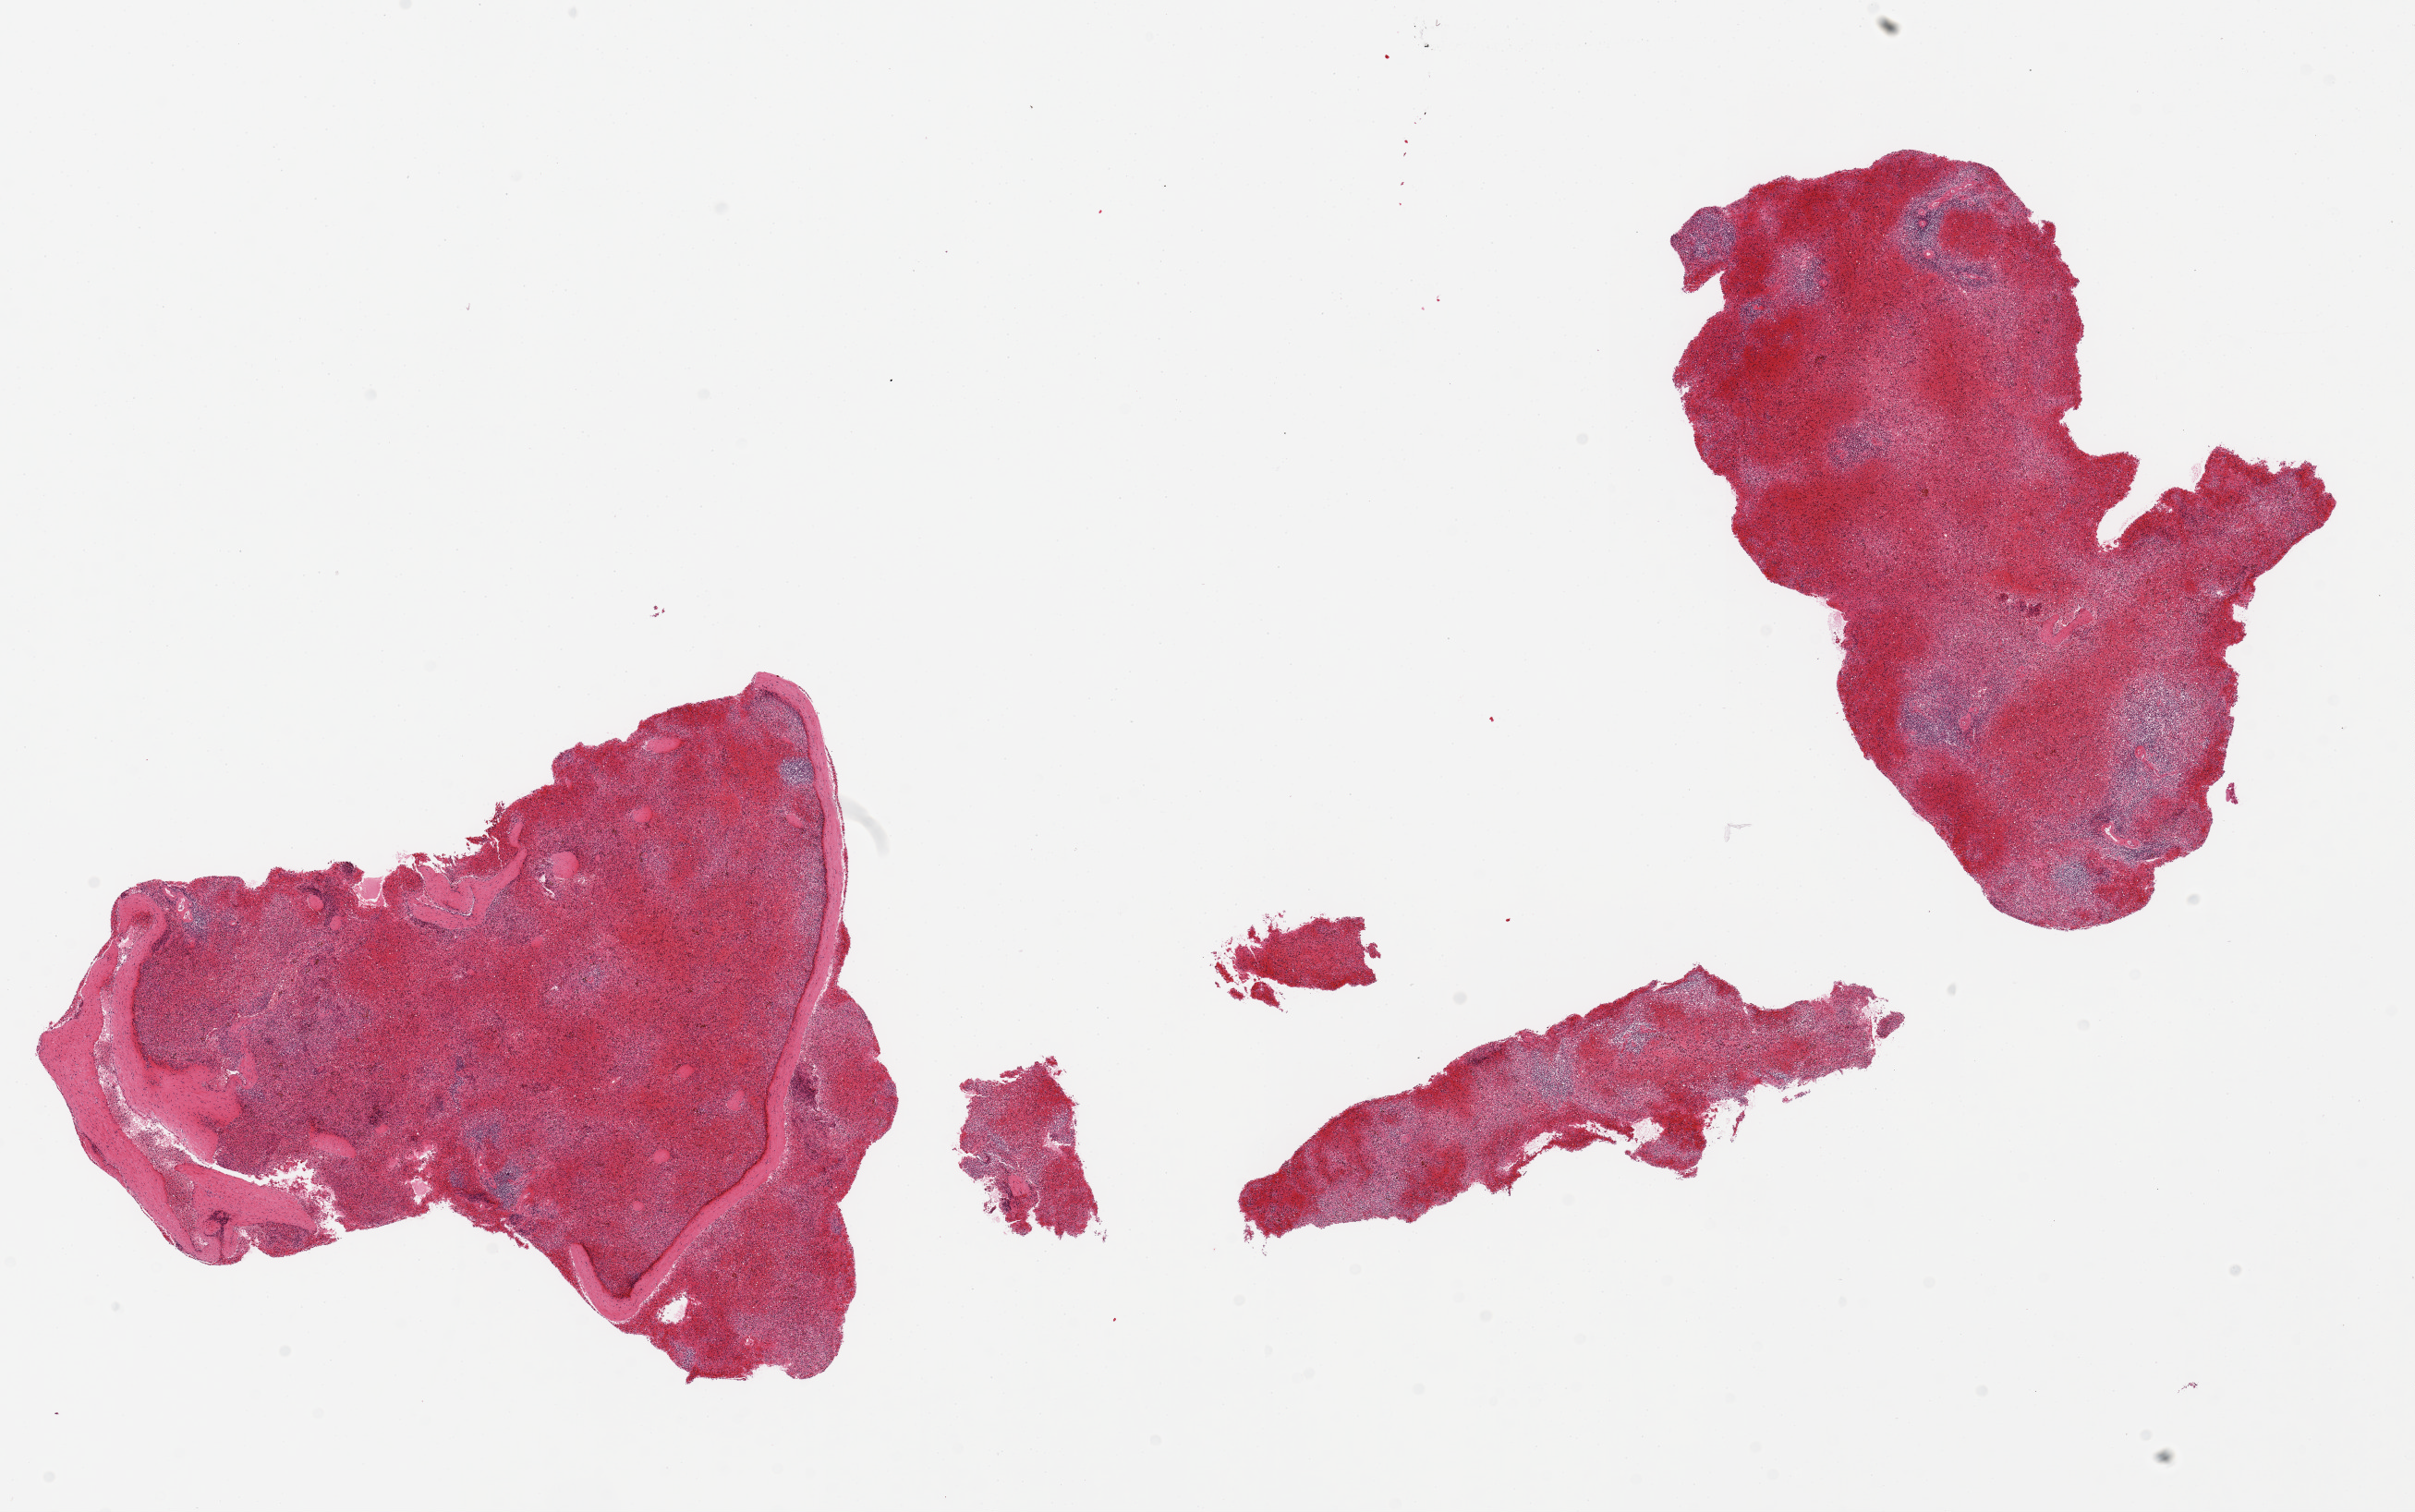
Whole-slide image, haematoxylin and eosin stain — low-resolution overview of the scanned area, about 20.7 x 12.9 mm, PAXgene-fixed paraffin-embedded (PFPE) section, section of spleen (target tissue), donor tissue sample. Male donor.
• pathologist's review note for this sample: 2 pieces, marked congestion and autolysis